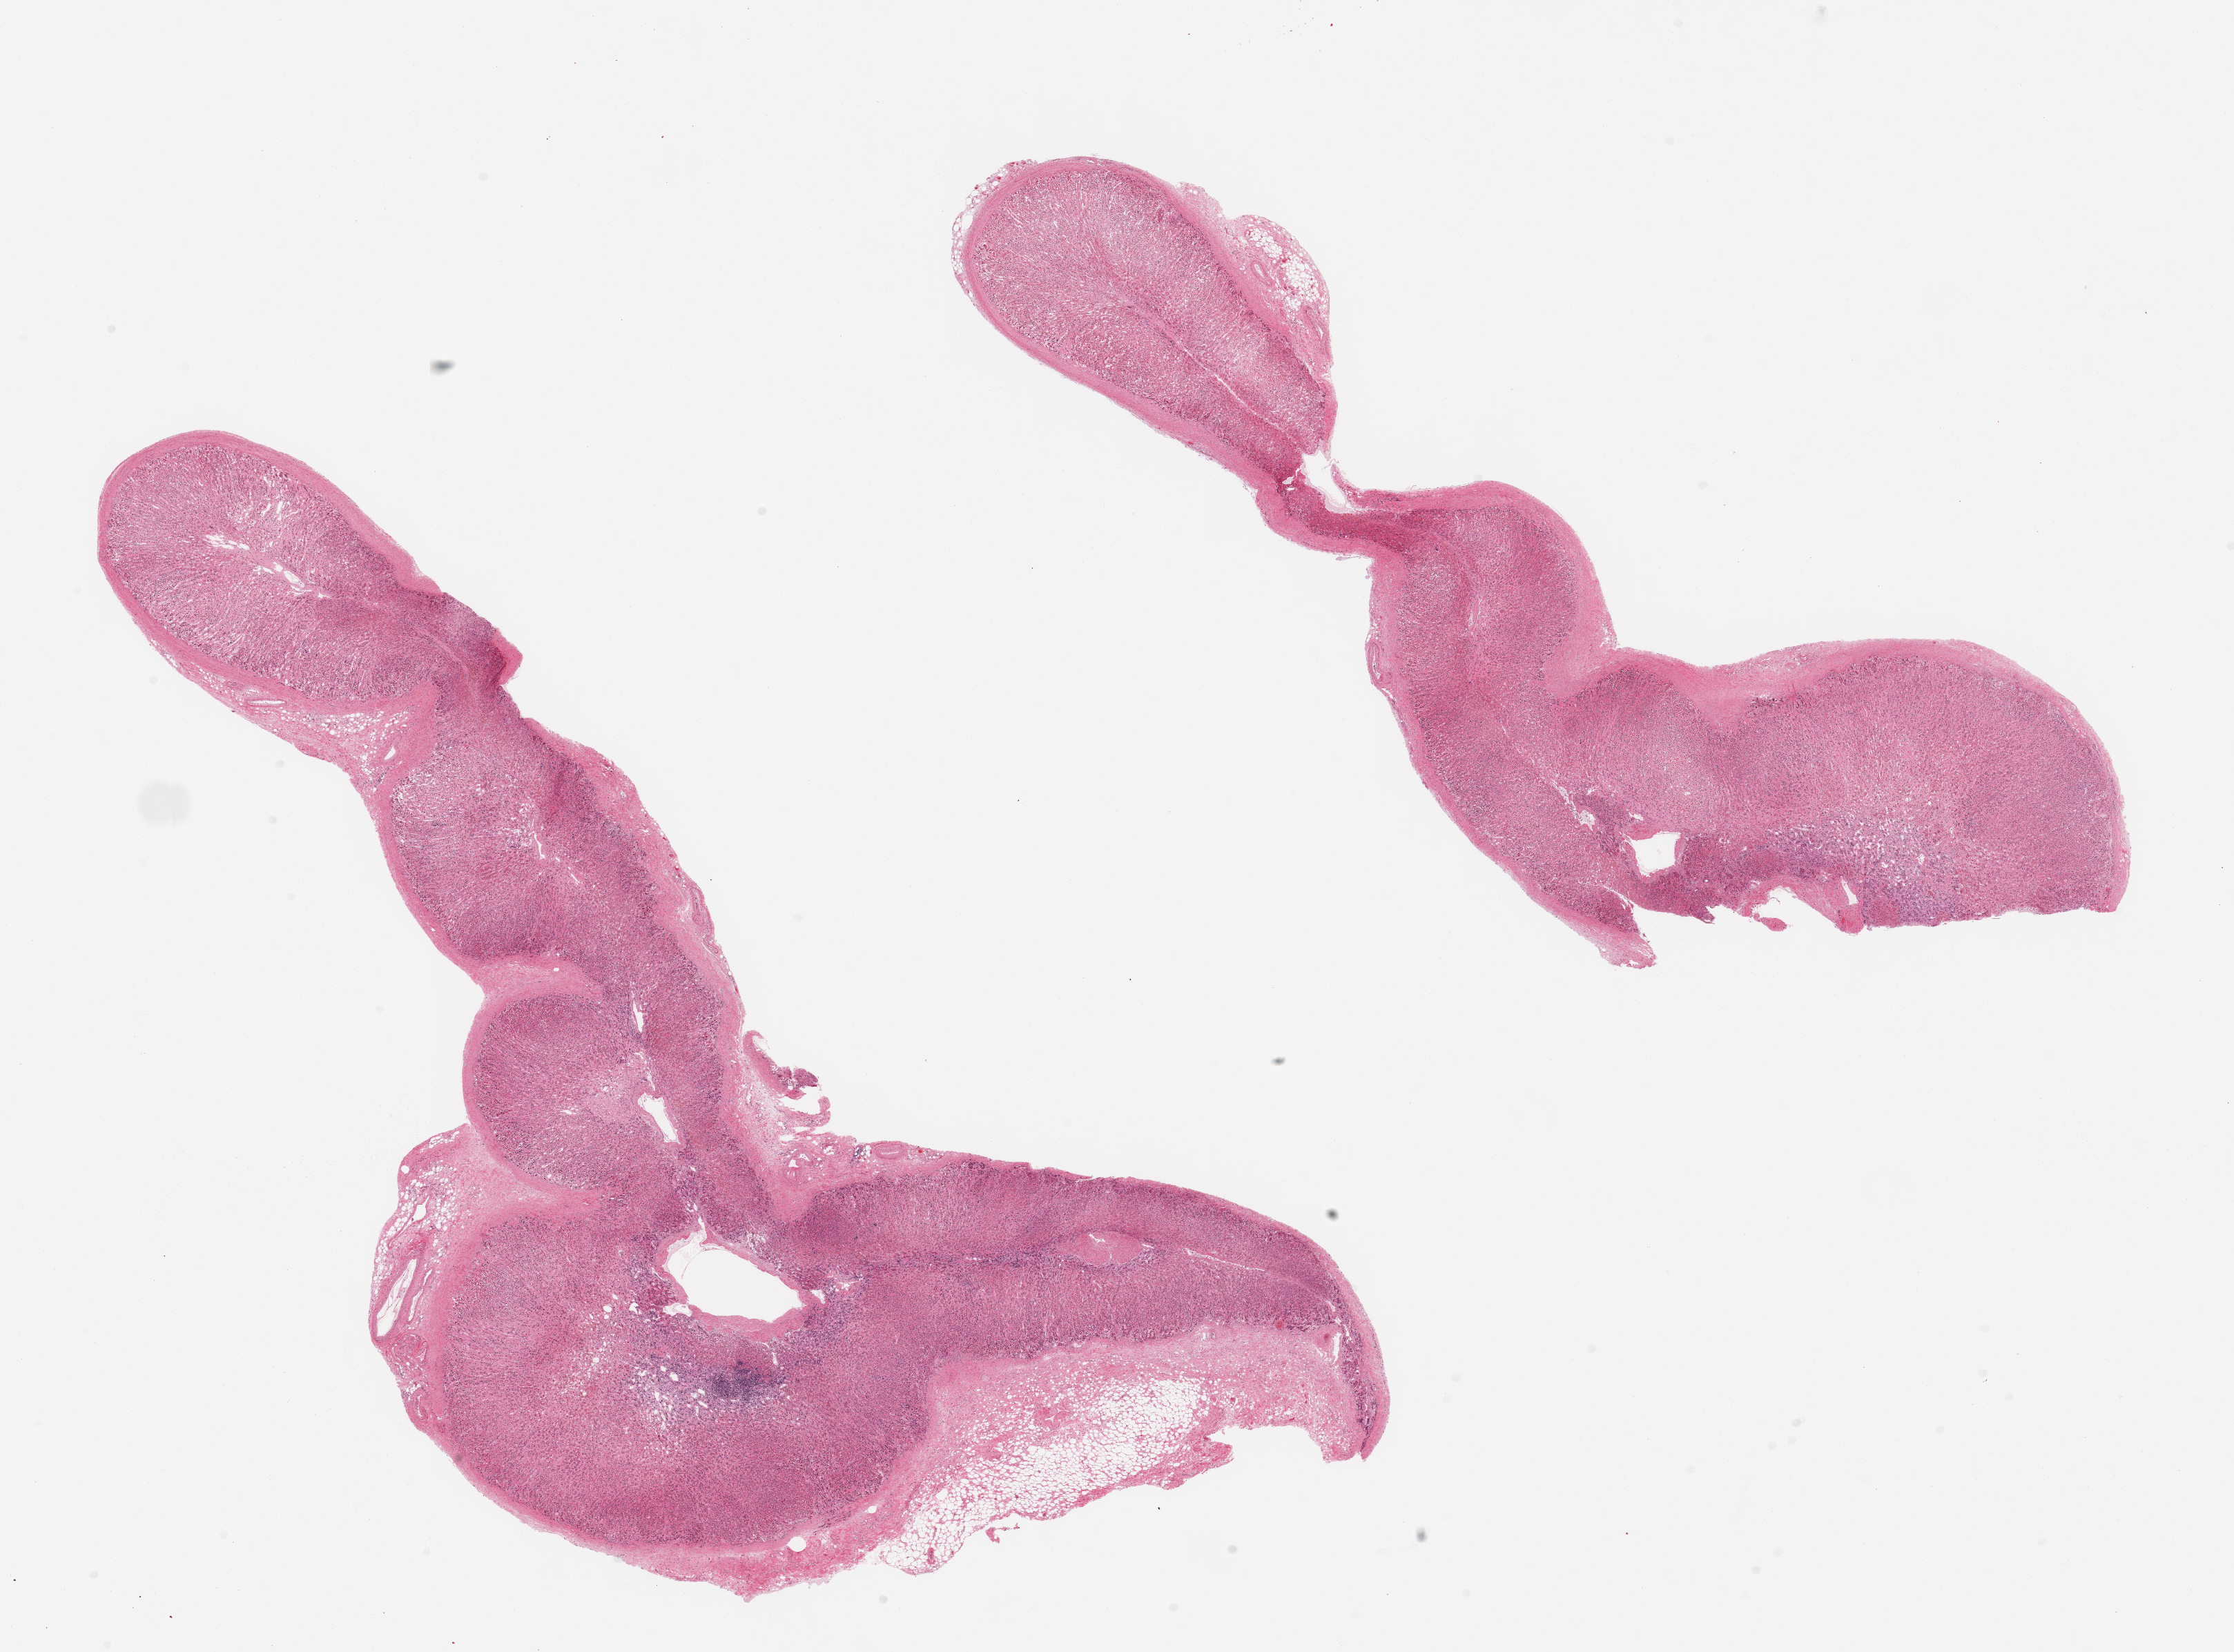
Whole-slide image, haematoxylin and eosin stain — a low-resolution overview of the entire scanned area, about 25.6 x 18.9 mm; PAXgene-fixed paraffin-embedded (PFPE) section; section of adrenal gland (target tissue); tissue donor sample. Donor: male.
Review note (as recorded): 2 pieces; moderate to severe autolysis; 10% & 20% external fat.